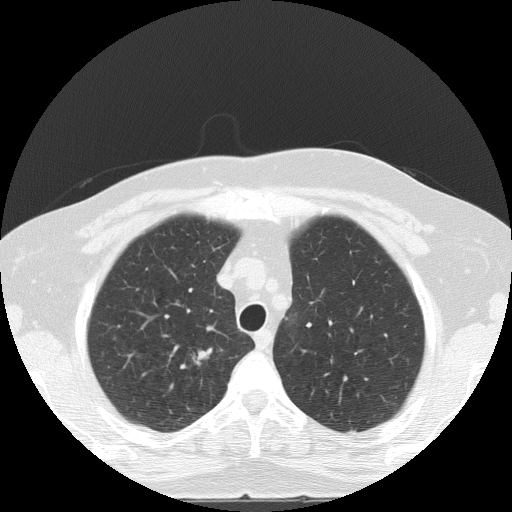
Low-dose screening chest CT, one axial slice; slice 107 of 133 in the series (ordered by position); reconstruction kernel FC51; 120 kVp; lung window (W 1500 / L -600 HU); 512 × 512 image matrix, field of view 320 × 320 mm.
Annotated regions visible in this slice (expert manual segmentation):
- lesion 1 (tumor, upper lobe of right lung): bounding box <197,349,211,360> (left, top, right, bottom; pixels)